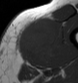
MRI of an extremity soft-tissue mass, one axial slice. Position 23 of 43 along the scan axis. MR volume resampled by the dataset authors to the PET/CT grid (not the native acquisition matrix). 78 × 83 image matrix. Male patient. Case-level facts recorded for this patient, not image findings: histological type: pleiomorphic leiomyosarcoma; grade: high; site of the primary tumour: left thigh.
Structures marked on this image (expert contour drawn on MRI and transferred to this co-registered scan by the dataset authors):
- gross tumour volume including surrounding oedema: bounding box (x1, y1, x2, y2) in pixels: (16, 19, 60, 64)
- gross tumour volume (mass): (18, 21, 55, 63)